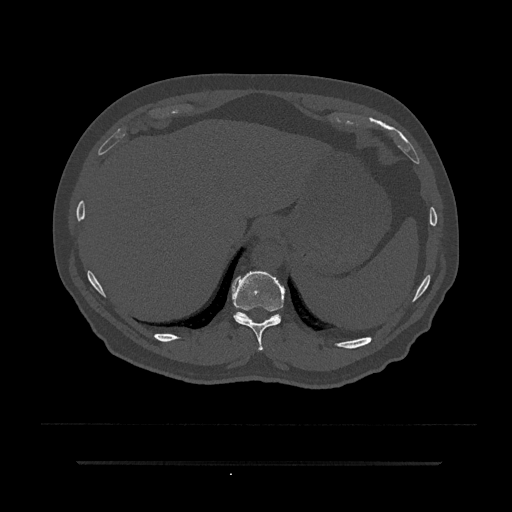
CT including the spine, one axial slice; position 312 of 797 along the scan axis; bone window (W 1800 / L 400 HU); 0.5 mm slice thickness; 512 × 512 image matrix, field of view 464 × 464 mm. Male patient, age 59 years. Case-level facts recorded for this patient, not image findings: primary cancer: bile ducts.
Outlined on this slice (semi-automatically segmented with operator editing):
- T10 vertebra: bounding box (x1, y1, x2, y2) in pixels: (232, 271, 285, 351)
- T11 vertebra: (235, 312, 281, 320)